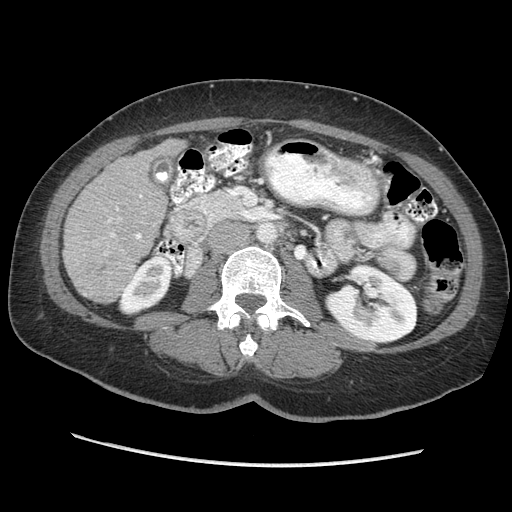
Contrast-enhanced abdominal CT (liver protocol), one axial slice. Slice 102 of 170 in the series (ordered by position). Reconstruction kernel STANDARD. Soft-tissue window (W 400 / L 40 HU). 2.5 mm slice thickness. 512 × 512 image matrix, field of view 360 × 360 mm. From the clinical record (not read from this slice): diagnosis: hepatocellular carcinoma (patient treated with transarterial chemoembolisation; whether this scan precedes or follows treatment is not stated here); TNM stage (as recorded): Stage-II; Child-Pugh class: A; tumour differentiation: no biopsy; tumour nodularity: multinodular.
Structures marked on this image (semi-automatic segmentation, software-assisted and operator-edited):
- liver parenchyma outside the tumour (the mass and vessels are separate outlines, so this box may not span the whole liver): box from (x=62, y=138) to (x=186, y=302) px
- liver vessels: (x=84, y=195)–(x=142, y=296)